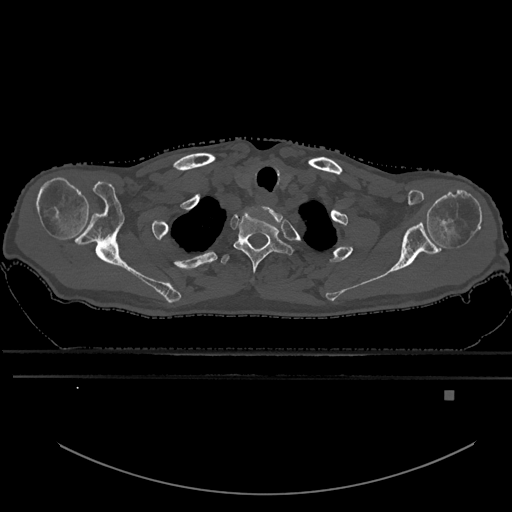
CT including the spine, one axial slice; slice 536 of 969 in the series (ordered by position); bone window (W 1800 / L 400 HU); 0.5 mm slice thickness; 512 × 512 image matrix. Patient: male, 82 years. Case-level facts recorded for this patient, not image findings: primary cancer: prostate.
Structures marked on this image (semi-automatic segmentation, software-assisted and operator-edited):
- T1 vertebra: bounding box [x1, y1, x2, y2] px = [233, 211, 292, 274]
- T2 vertebra: [220, 254, 231, 265]